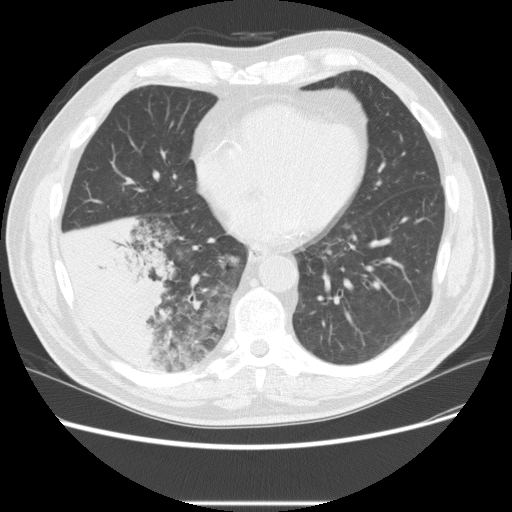
Low-dose screening chest CT, one axial slice; 120 kVp; lung window (W 1500 / L -600 HU); 2.5 mm slice thickness; 512 × 512 image matrix, field of view 380 × 380 mm.
Outlined on this slice (manually delineated by an expert):
- lesion 3 (tumor, lower lobe of right lung): bounding box <58,214,177,366> (left, top, right, bottom; pixels)